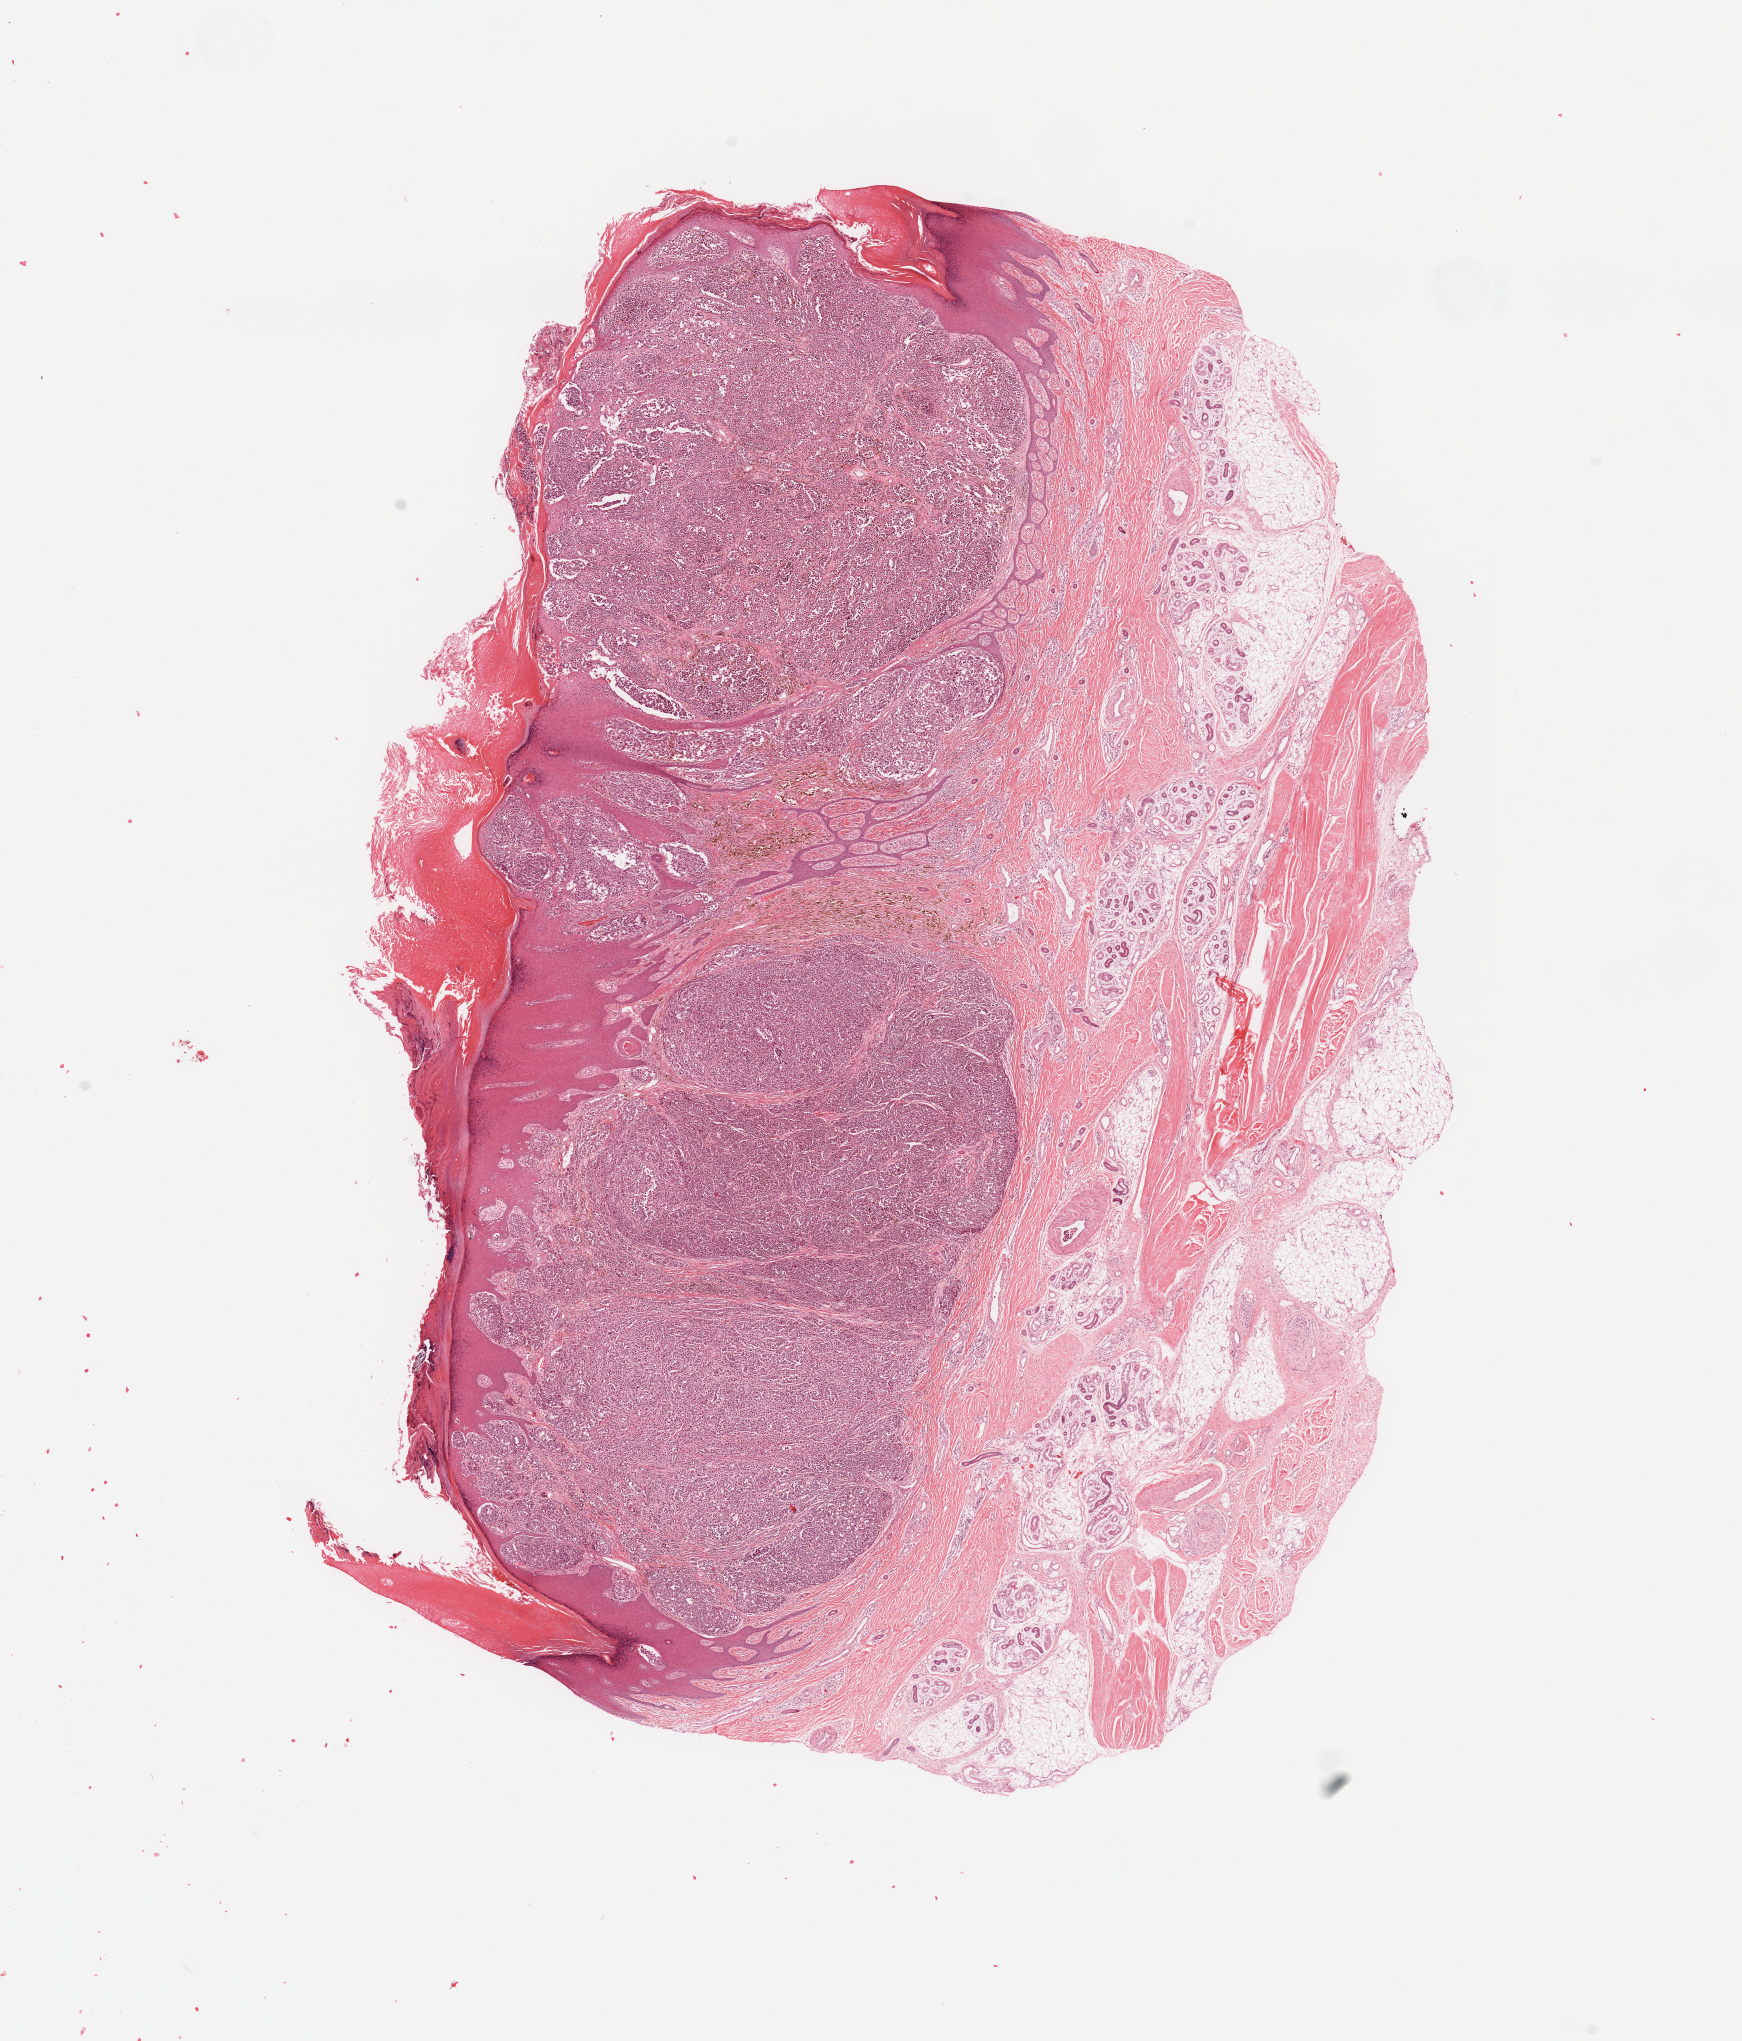
Digitized H&E tissue section (whole slide), whole scanned area (about 13.8 x 16.1 mm, from a 20x scan) shown as a low-resolution overview; melanoma tumour tissue; sampled site not recorded. 69-year-old male patient.
AJCC pathologic stage: IIIC. Histologic diagnosis: Malignant melanoma, NOS.